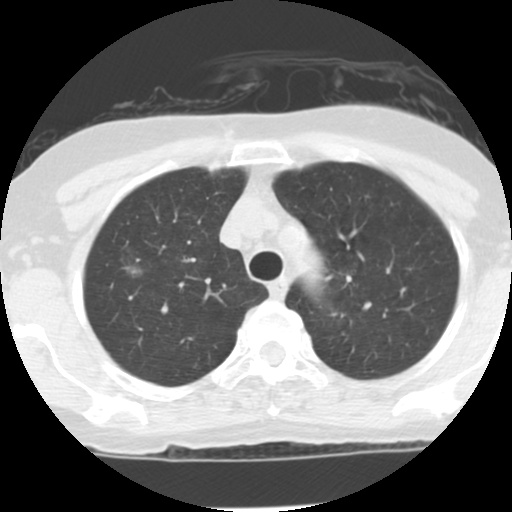
Chest CT (low-dose screening protocol), one axial image. Third annual screen. Lung window (W 1500 / L -600 HU). 2.5 mm slice thickness. Slice 25 of 122 in the series. Female participant, aged 62 years at enrolment.
- Lesion marked by an expert reader, bounding box (x1, y1, x2, y2) in pixels: (112, 251, 157, 294).
- Screening reader's record for this exam (one nodule recorded; not confirmed to be the boxed lesion): non-calcified nodule or mass ≥4 mm, right upper lobe, 9 × 8 mm, poorly defined margins, ground glass attenuation, pre-existing on the prior screen: yes; interval growth: yes.
- Official screen result: positive, other.
- Later outcome: lung cancer diagnosed 134 days after this screen — bronchiolo-alveolar adenocarcinoma, NOS, right upper lobe, stage IA (AJCC 6th edition), 10 mm at pathology.